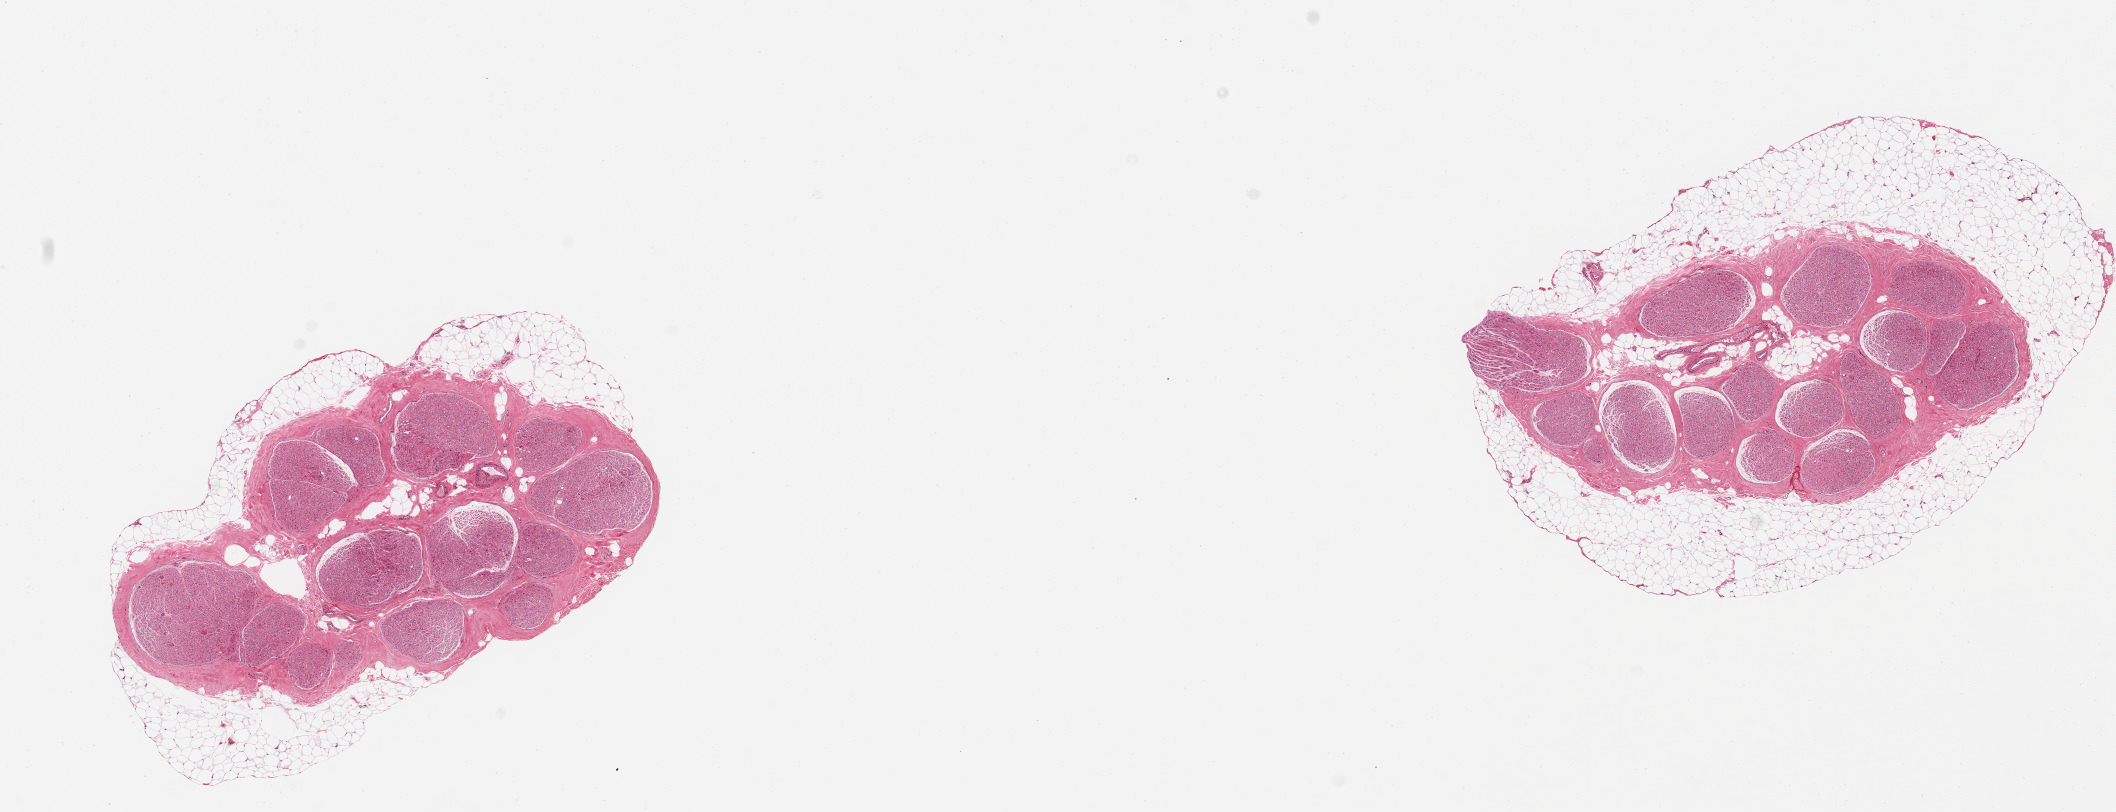
Whole-slide image, H&E stain, a low-resolution overview of the entire scanned area, about 16.7 x 6.4 mm. PAXgene-fixed paraffin-embedded (PFPE) section. Sampled site (target tissue): tibial nerve. Donor tissue sample. Donor sex: female.
* review note (as recorded): 2 pieces; 20 & 40% external untrimmed fat